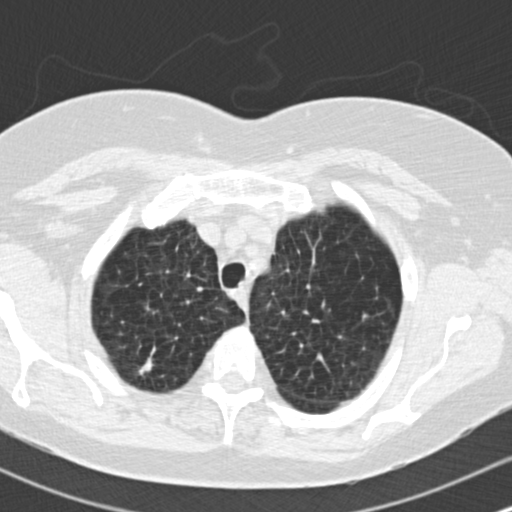
Chest CT (low-dose screening protocol), one axial image, baseline annual screen, lung window (W 1500 / L -600 HU), 2 mm slice thickness, standard (soft-tissue) reconstruction kernel (B30f). Female, age 73 years at enrolment. Former smoker at enrolment.
• Expert-annotated lung lesion, box from (x=120, y=341) to (x=173, y=387) px.
• The screening reader recorded 2 non-calcified nodules or masses ≥4 mm on this exam (right upper lobe, right upper lobe); which of them this box marks is not recorded.
• Official screen result: positive, change unspecified: nodule(s) >= 4 mm or enlarging nodule(s), mass(es), or other non-specific abnormalities suspicious for lung cancer.
• Later outcome: lung cancer diagnosed 601 days after this screen — adenocarcinoma, NOS, right upper lobe, moderately differentiated (G2), stage IB (AJCC 6th edition), 15 mm at pathology.